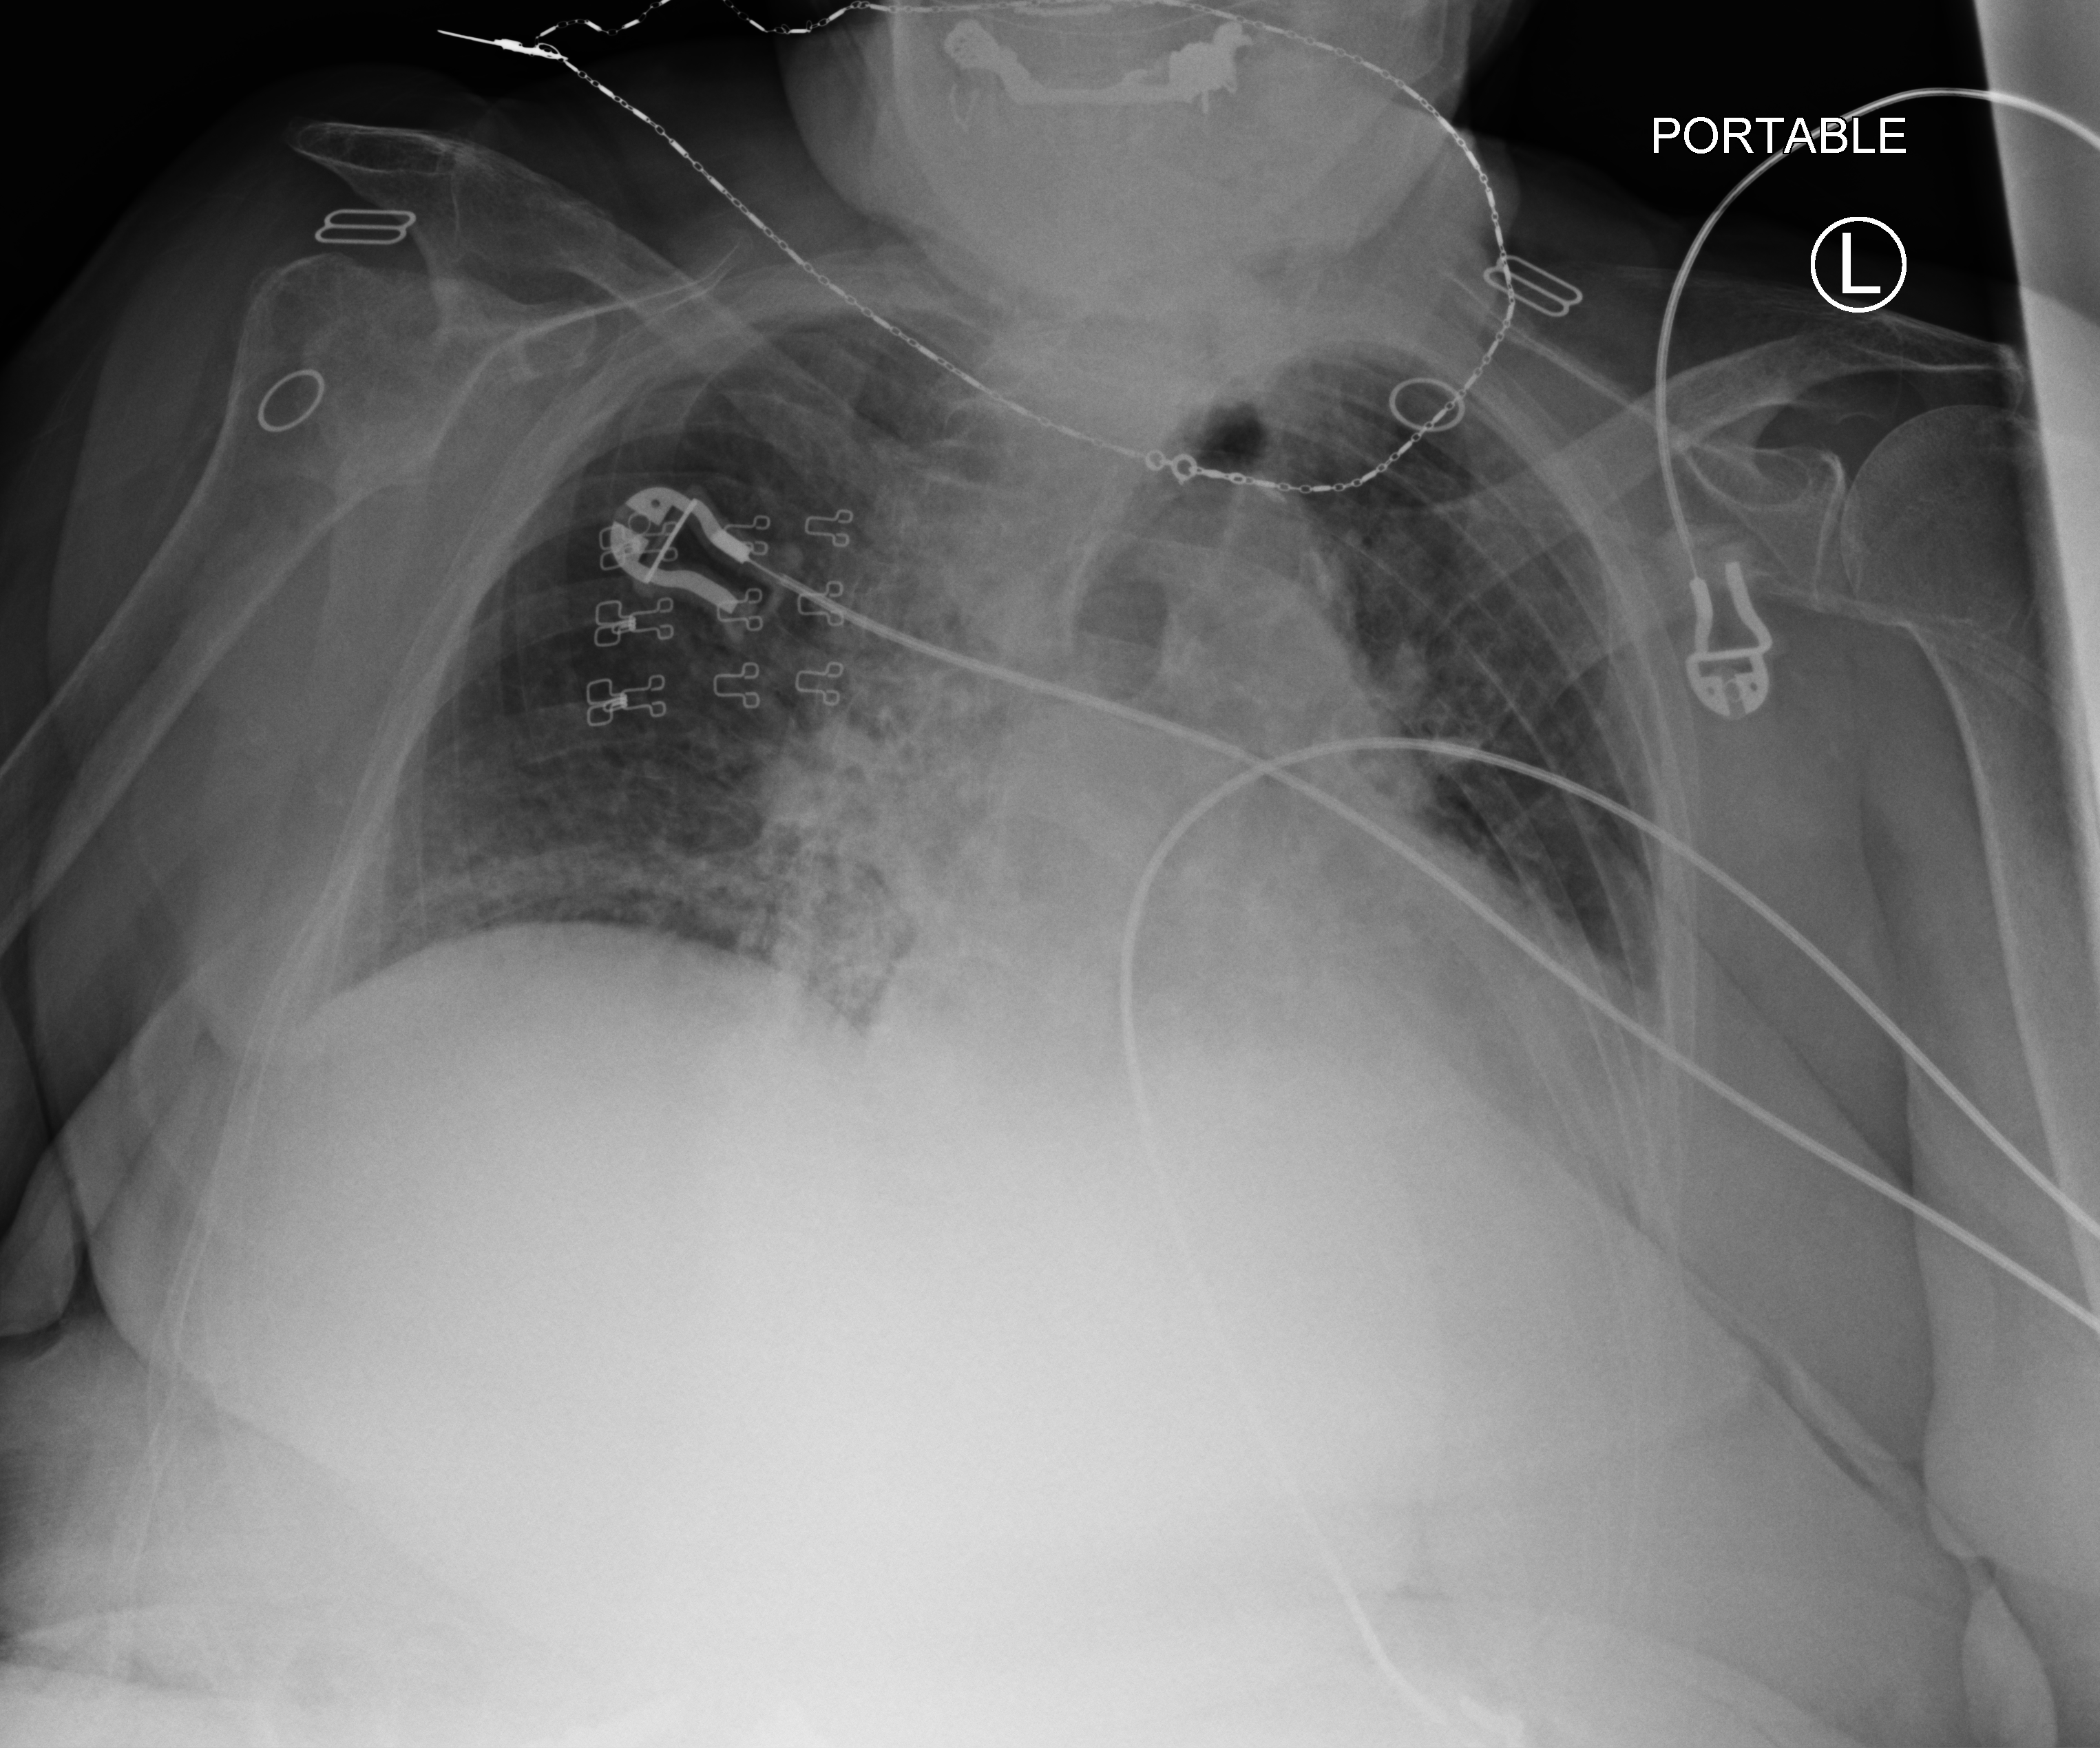
Bedside chest radiograph (computed radiography), anteroposterior (AP) projection. Patient hospitalised with COVID-19; female, aged 75–90 years.
Admission-level facts for this patient (not findings on this image; timing relative to this image not recorded): admitted to intensive care during this hospital stay: no.